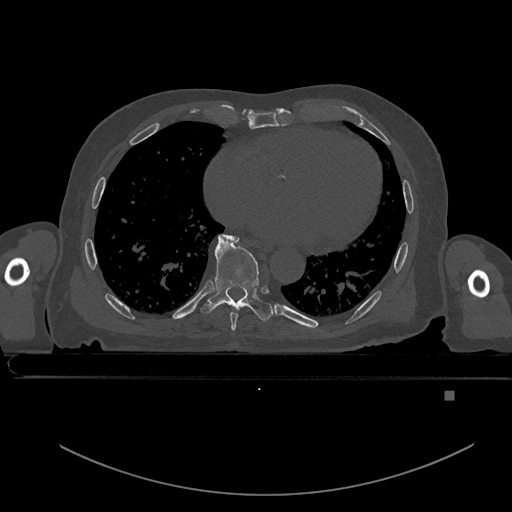
CT including the spine, one axial slice. Position 215 of 969 along the scan axis. Bone window (W 1800 / L 400 HU). 512 × 512 image matrix, field of view 456 × 456 mm. Patient: male, 82 years. Case-level facts recorded for this patient, not image findings: primary cancer: prostate; vertebrae with lytic lesions (as recorded): T11, T9, T8, T2.
Outlined on this slice (semi-automatic segmentation, software-assisted and operator-edited):
- T7 vertebra: bounding box <226,236,238,330> (left, top, right, bottom; pixels)
- T8 vertebra: <201,234,273,321>